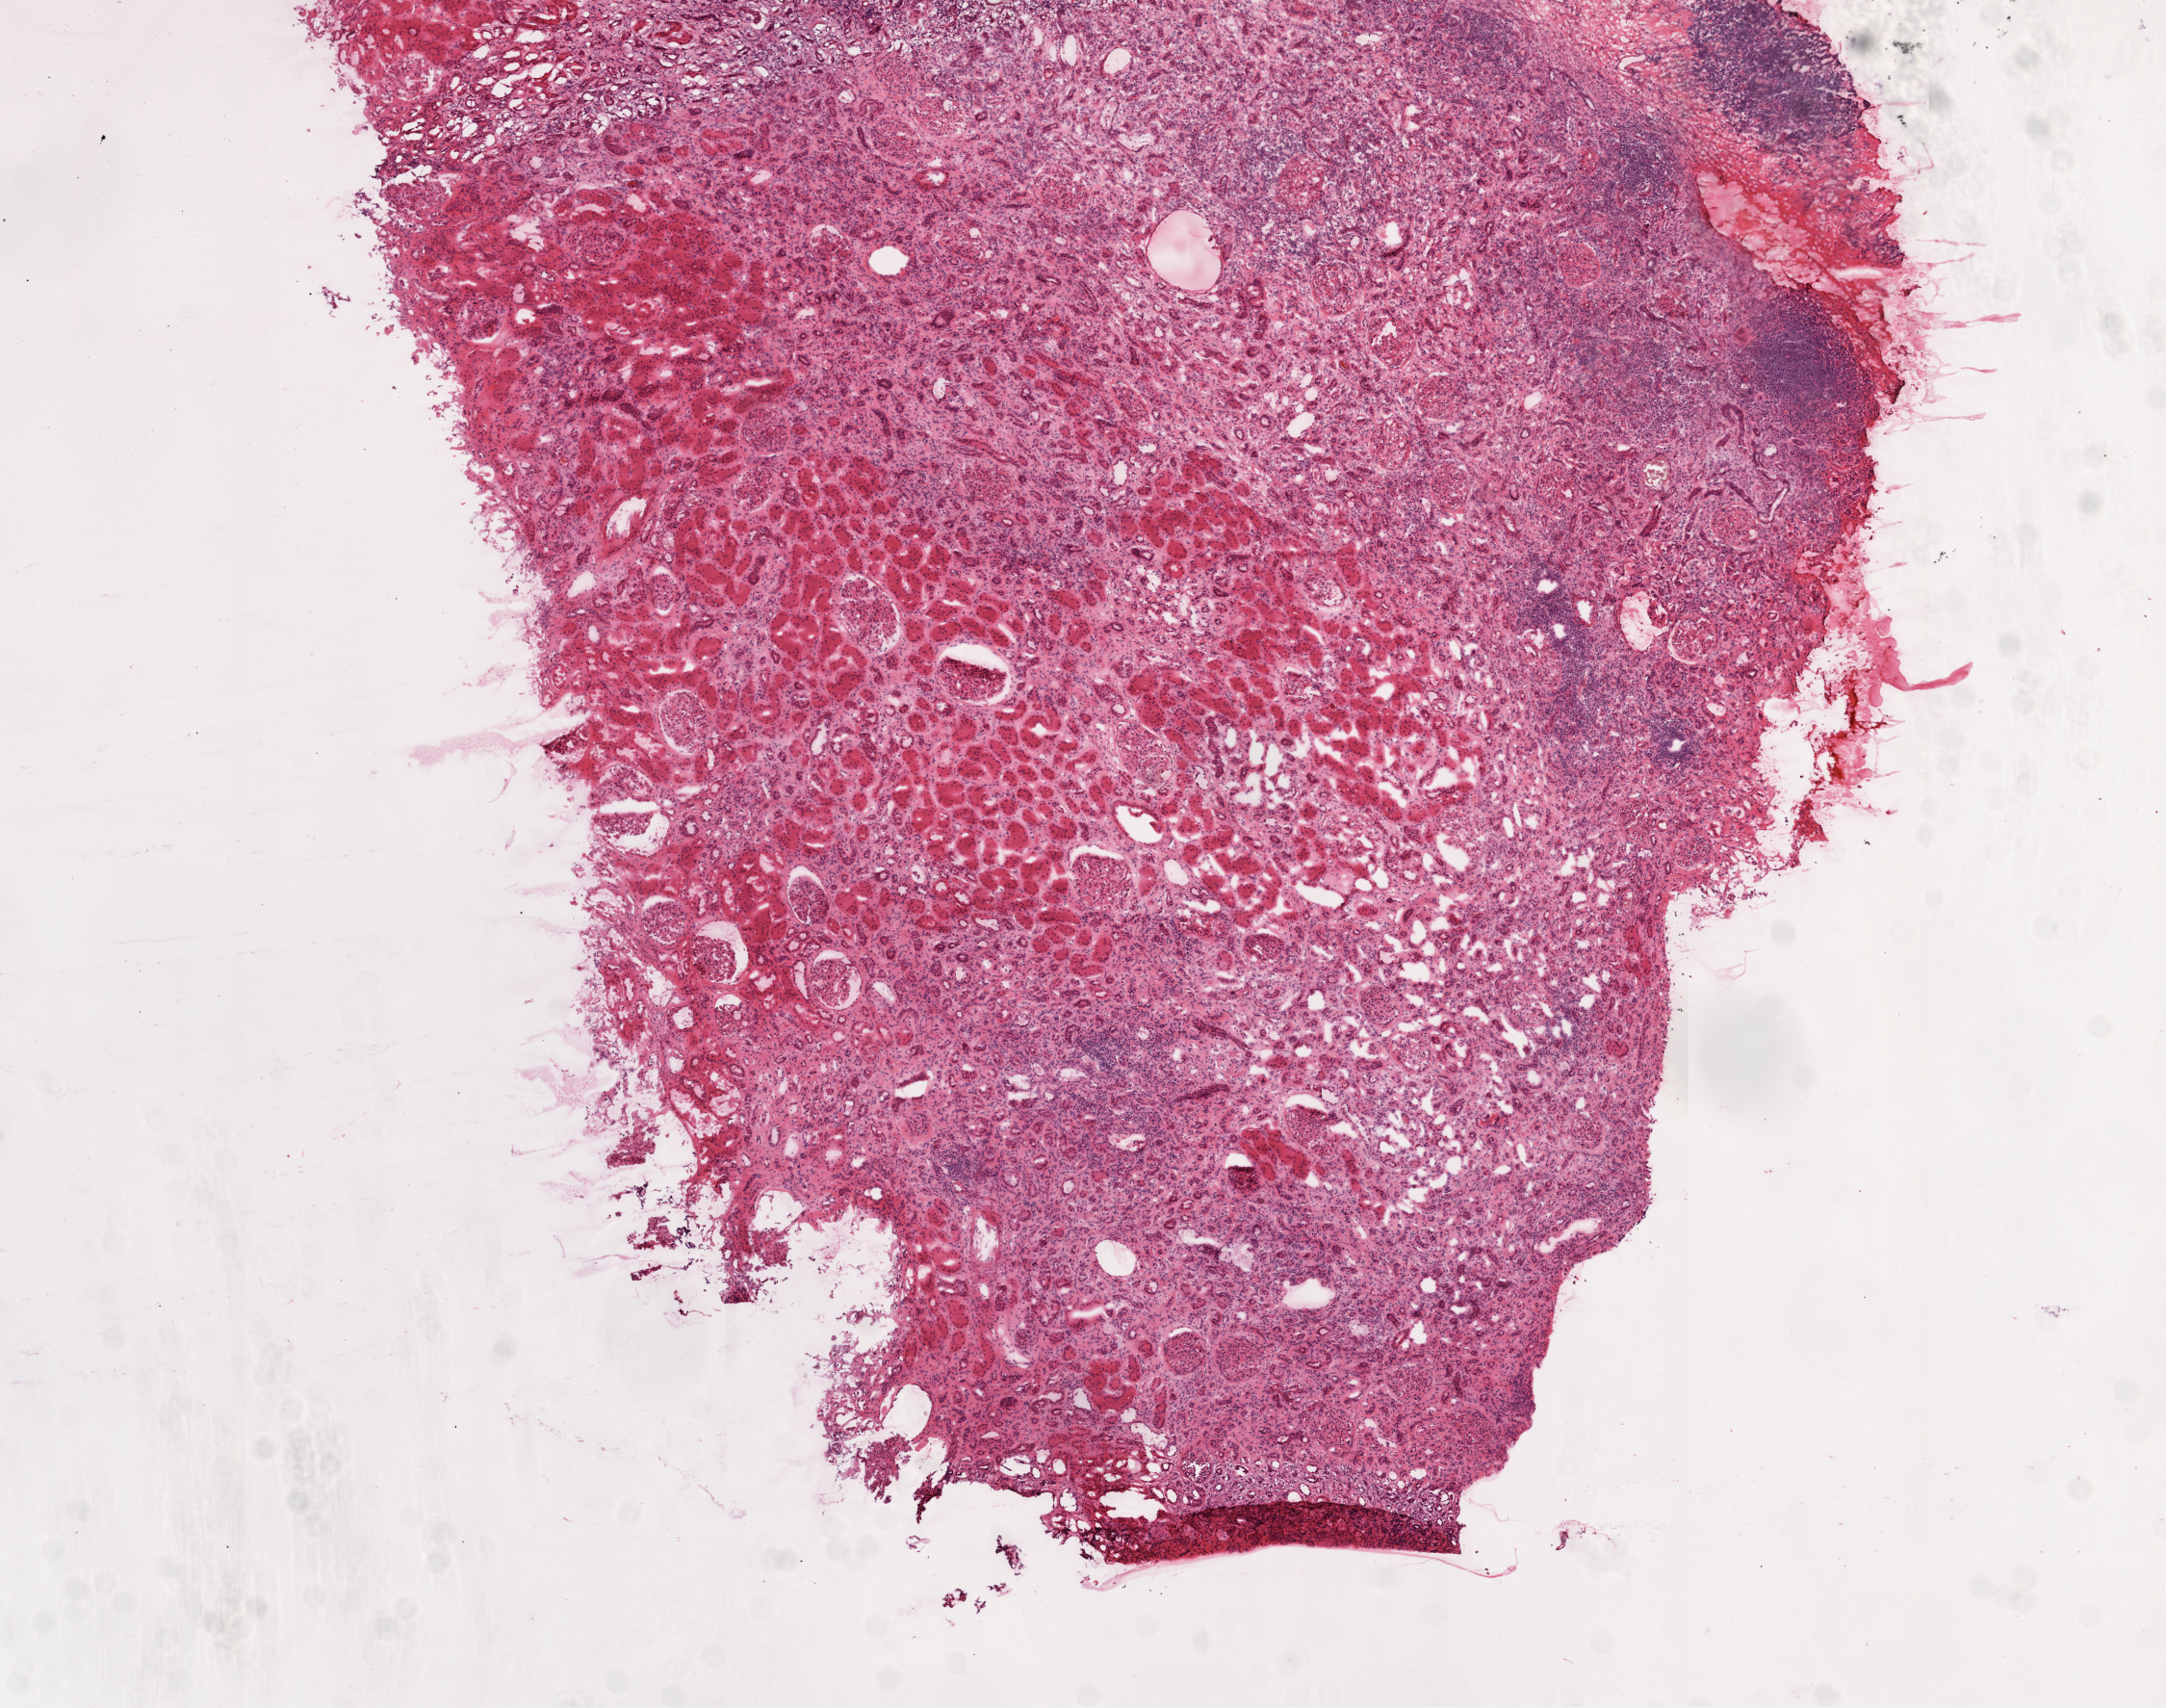
Digitized H&E tissue section (whole slide) — whole scanned area (about 9.0 x 7.1 mm, slide scanned at 20x) shown as a low-resolution overview. Frozen section. Sample: solid tissue normal (non-tumour tissue), kidney. Male, age 52 years at initial diagnosis.
This section: solid tissue normal sample (biorepository sample class). Patient diagnosis: Clear cell adenocarcinoma, NOS.